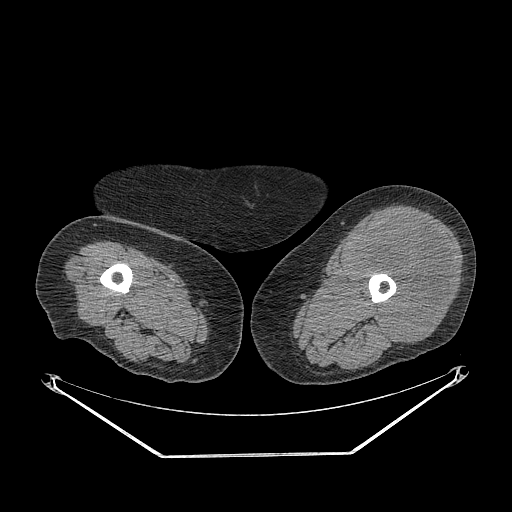
CT of an extremity soft-tissue mass (from a PET/CT study), one axial slice; reconstruction kernel STANDARD; soft-tissue window (W 400 / L 40 HU); 512 × 512 image matrix, field of view 500 × 500 mm. Female patient. Case-level facts recorded for this patient, not image findings: histological type: undifferentiated – high grade; grade: high; site of the primary tumour: left thigh.
Annotated regions visible in this slice (expert contour drawn on MRI and transferred to this co-registered scan by the dataset authors):
- gross tumour volume including surrounding oedema: bounding box <354,215,453,341> (left, top, right, bottom; pixels)
- gross tumour volume (mass): <354,215,453,341>